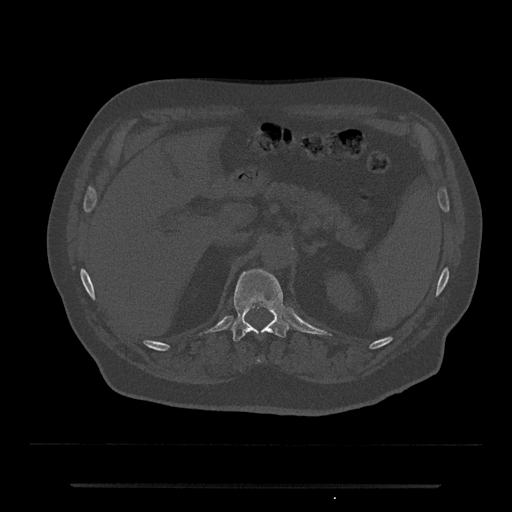
CT including the spine, one axial slice; position 598 of 797 along the scan axis; reconstruction kernel Br40s/3; 120 kVp; bone window (W 1800 / L 400 HU); 0.5 mm slice thickness; 512 × 512 image matrix, field of view 434 × 434 mm. Patient: male, 80 years. Case-level facts recorded for this patient, not image findings: primary cancer: prostate; vertebrae with lytic lesions (as recorded): L1, T11.
Annotated regions visible in this slice (semi-automatically segmented with operator editing):
- T12 vertebra: box from (x=230, y=269) to (x=290, y=342) px